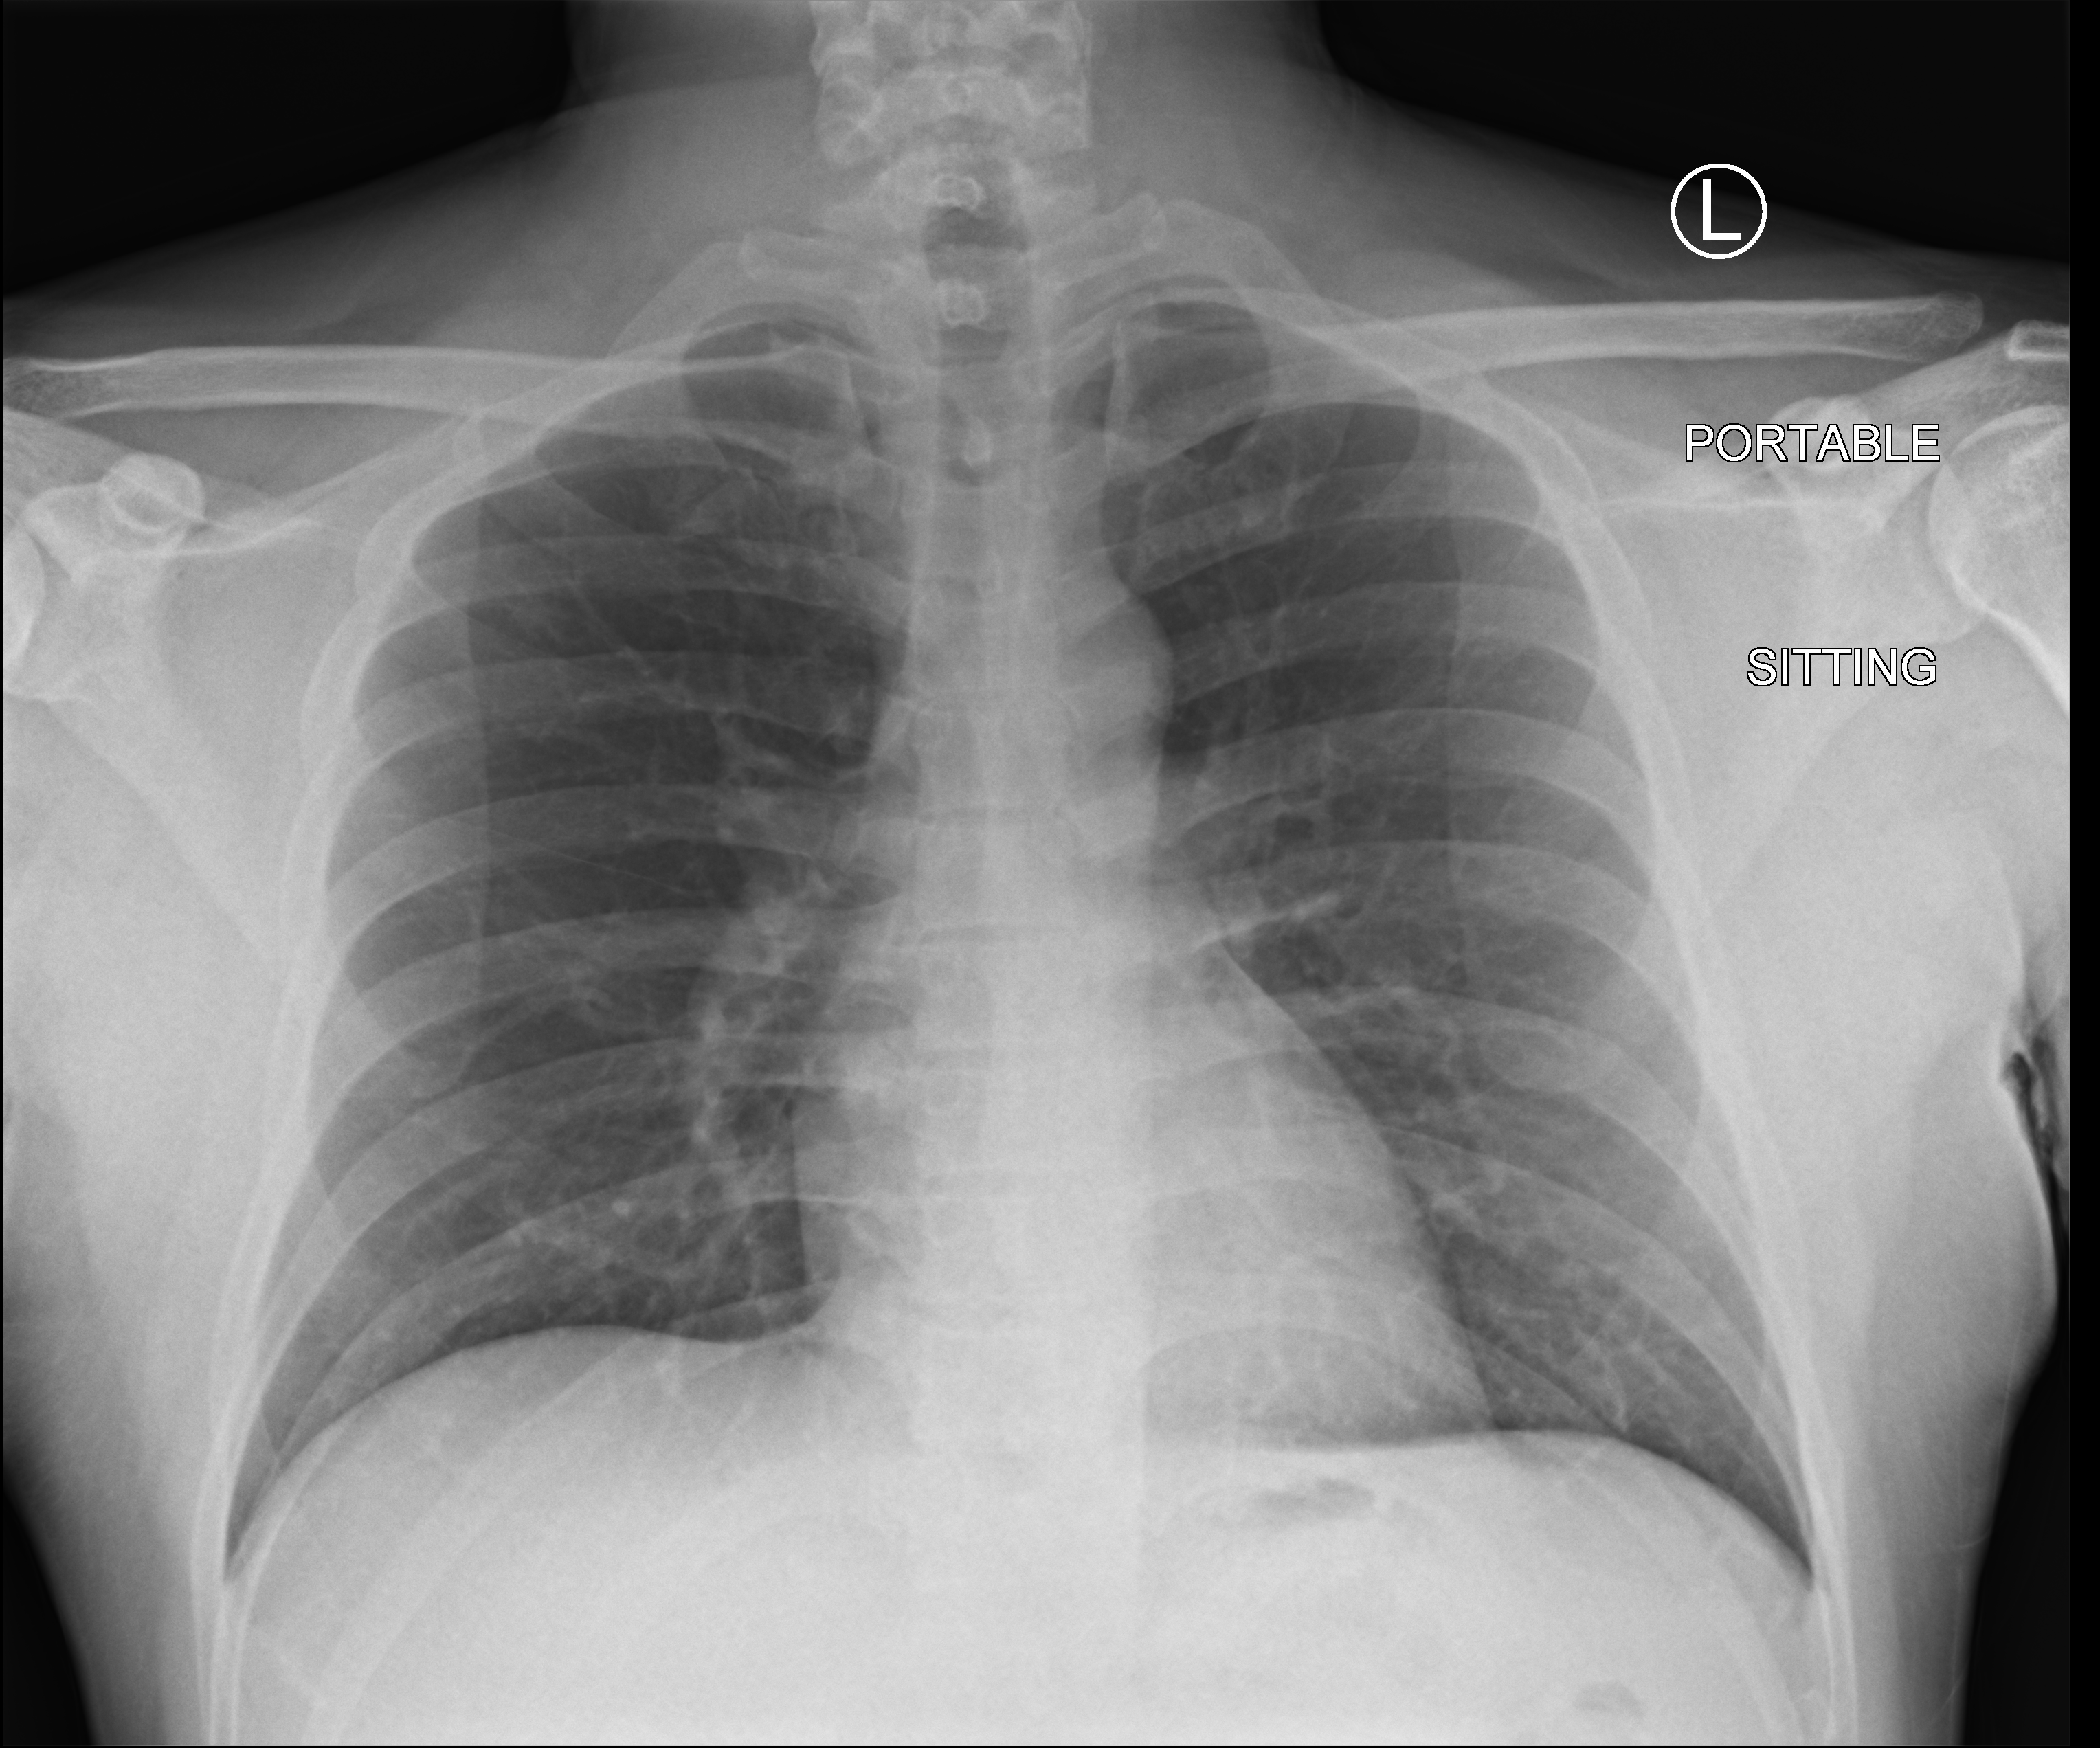
Bedside chest radiograph (computed radiography). Patient hospitalised with COVID-19; male, aged 18–59 years.
Hospital-stay facts (about this admission, not read from this image; timing relative to this image not recorded):
- other chronic lung disease (admission record): no
- smoking status (admission record): never